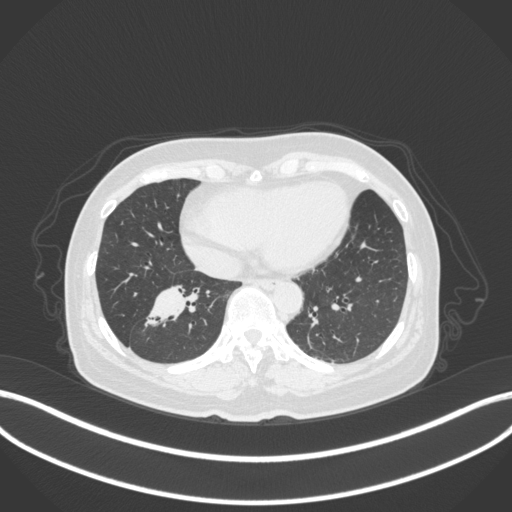
Chest CT, one axial slice; position 131 of 429 along the scan axis; lung window (W 1500 / L -600 HU); 1 mm slice thickness; 512 × 512 image matrix, field of view 400 × 400 mm. Female patient, age 67 years. From the clinical record (not read from this slice): clinical TNM (as recorded): T1c N1 M0; histopathological grade: G2-3.
Structures marked on this image (rectangle marked by the reading radiologist):
- lung tumour (recorded histology: adenocarcinoma): bounding box (x1, y1, x2, y2) in pixels: (140, 279, 203, 336)